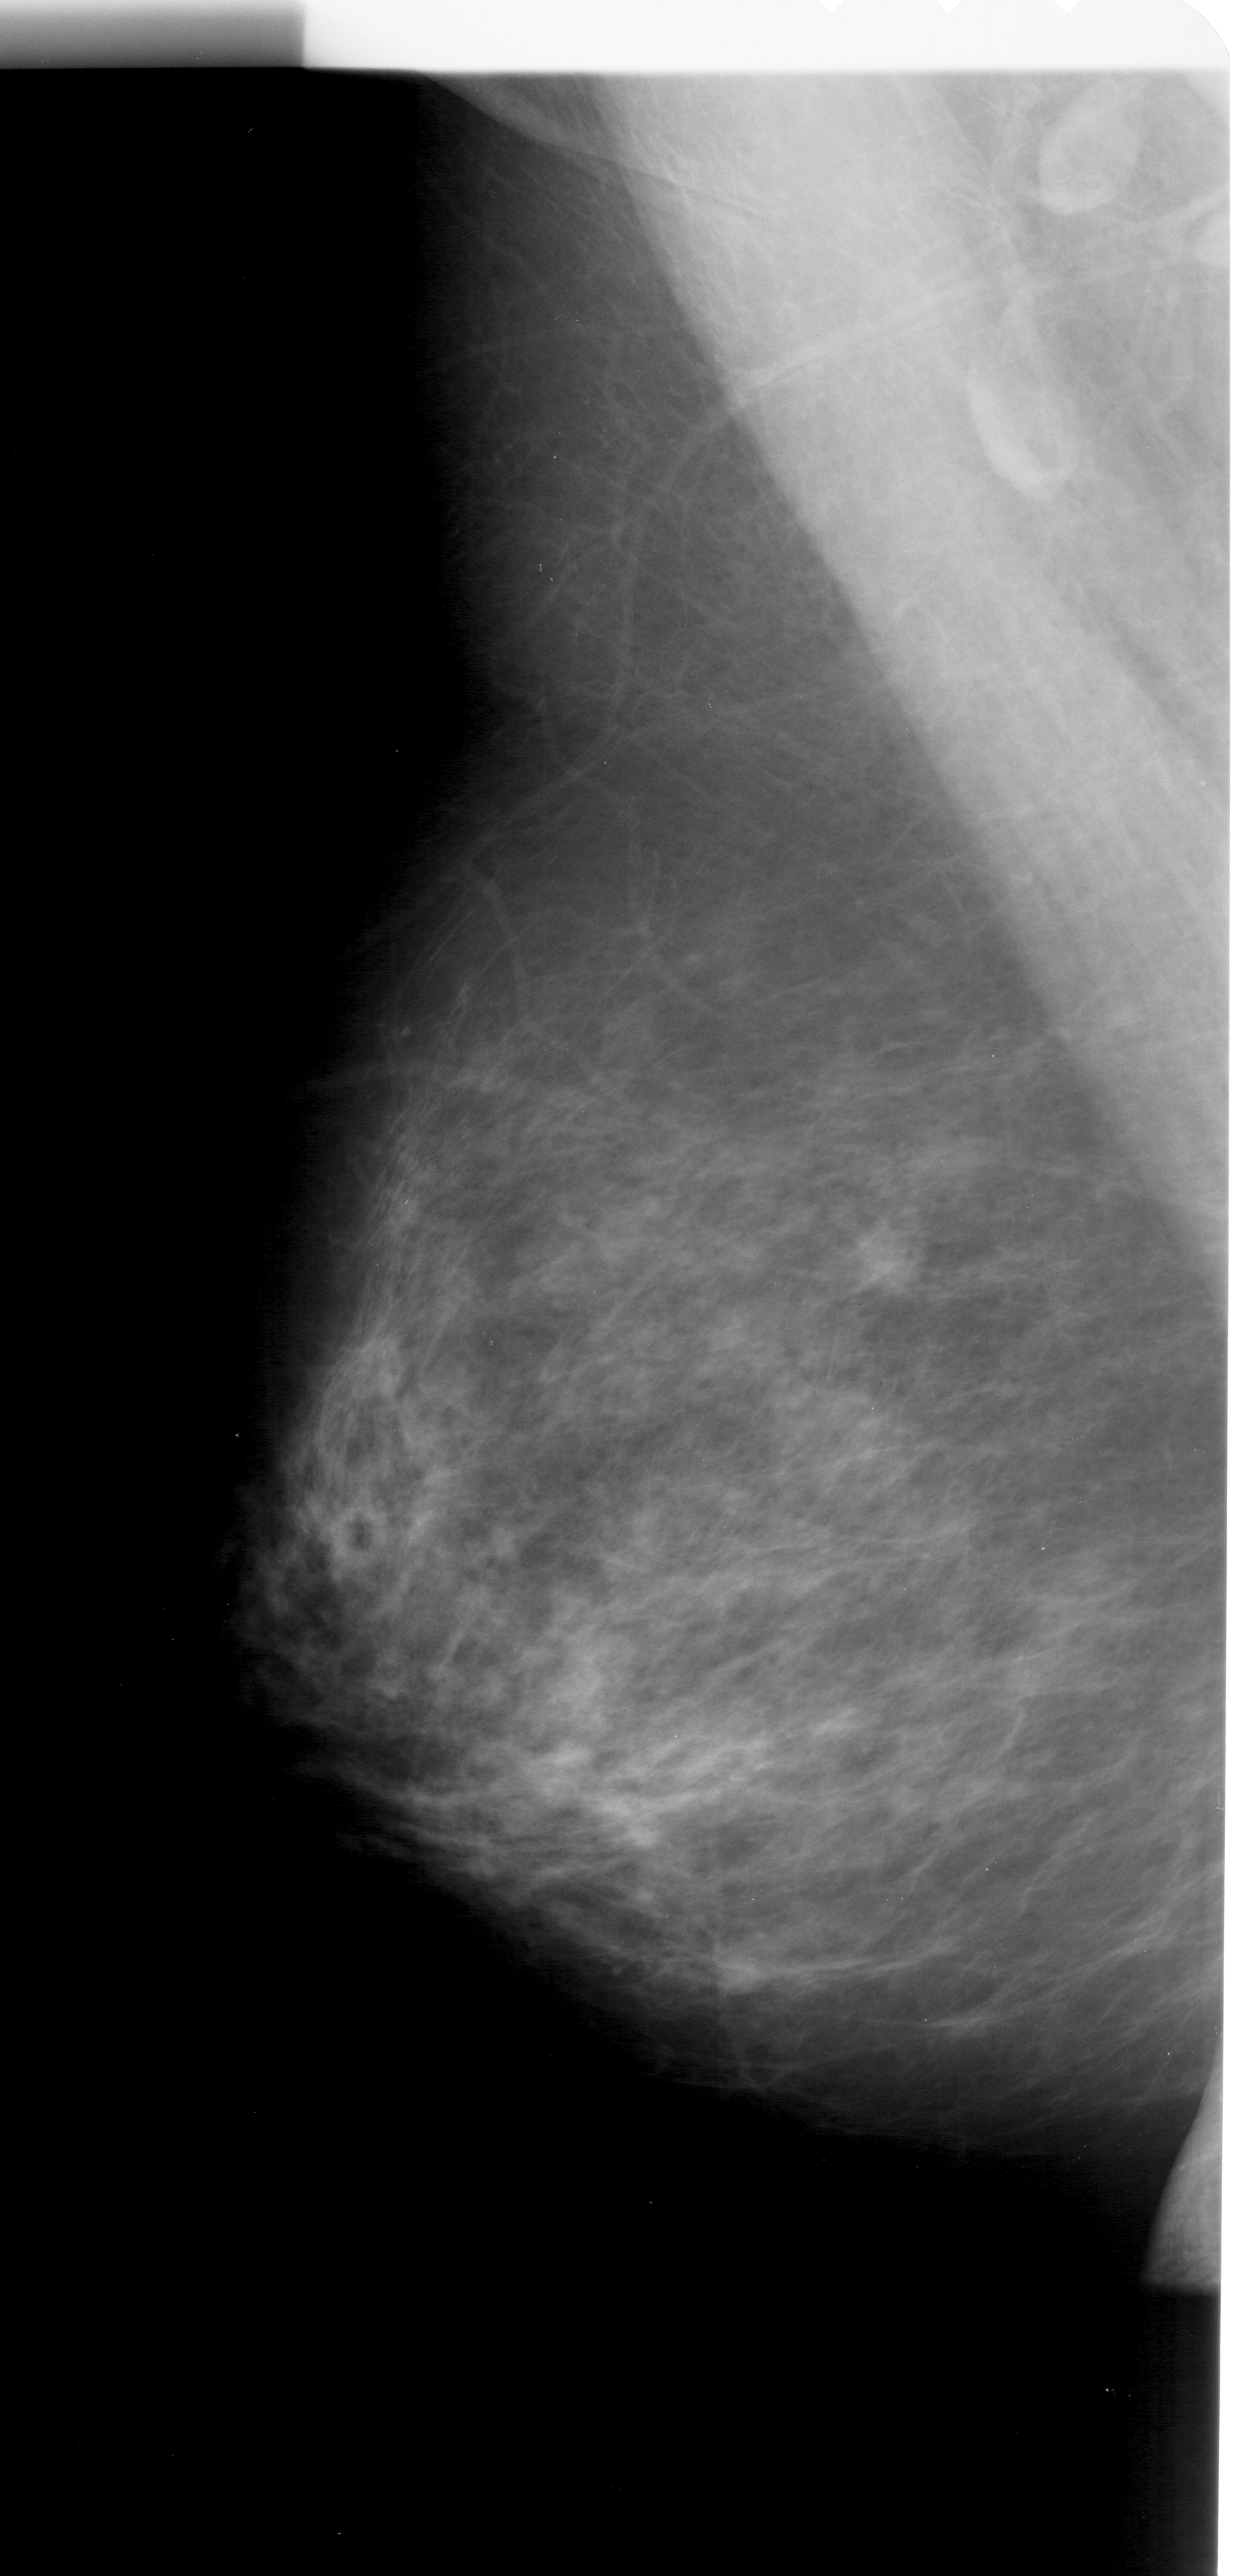
Scanned film-screen mammogram. Left breast. MLO view. 1241 × 2576 image matrix.
Expert-marked regions of interest on this film, with their recorded descriptors:
- mass, shape irregular, margins ill defined; BI-RADS assessment category 4; pathology (as recorded): malignant: box from (x=836, y=1214) to (x=927, y=1302) px